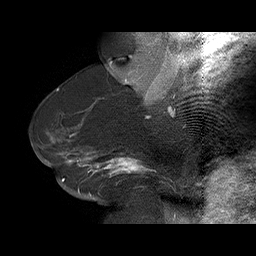
Breast MRI (dynamic contrast-enhanced), one sagittal slice. Position 42 of 75 along the scan axis. Dynamic contrast-enhanced series, time point 2 of 6 at this slice position (early post-contrast). 1.5 T. TE 4.5 ms, TR 32.4 ms. 256 × 256 image matrix, field of view 180 × 180 mm. Female patient. Case-level facts recorded for this patient, not image findings: setting: breast cancer imaged before/during neoadjuvant chemotherapy; receptor status: HR-positive, HER2-negative.
Outlined on this slice (semi-automatic segmentation, software-assisted and operator-edited):
- analysis volume of interest (the breast-tissue region the enhancement analysis was run in; not a lesion): bounding box <58,134,166,191> (left, top, right, bottom; pixels)
- tumour enhancement mask (voxels above the 100 % enhancement threshold inside the analysis volume of interest): <61,134,154,181>